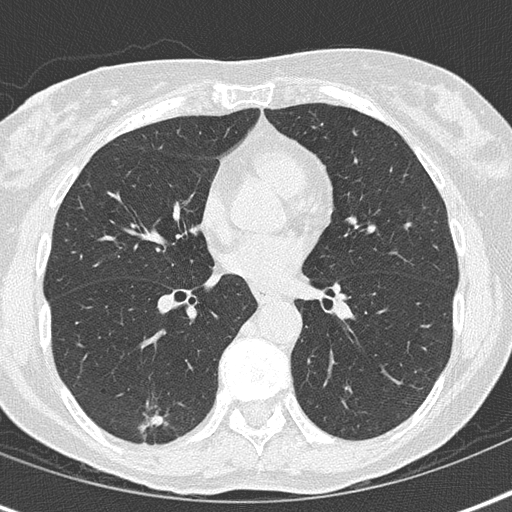
Low-dose screening chest CT, axial slice, baseline annual screen, lung window (W 1500 / L -600 HU), 2 mm slice thickness, lung (sharp) reconstruction kernel (B50f), slice 85 of 155 in the series. Female, age 69 years at enrolment.
- Expert reader's lesion annotation, bounding box (x1, y1, x2, y2) in pixels: (117, 399, 180, 456).
- The screening reader recorded 2 non-calcified nodules or masses ≥4 mm on this exam; which of them this box marks is not recorded.
- Official screen result: positive, change unspecified: nodule(s) >= 4 mm or enlarging nodule(s), mass(es), or other non-specific abnormalities suspicious for lung cancer.
- Later outcome: lung cancer diagnosed 476 days after this screen — adenocarcinoma, NOS, right lower lobe, moderately differentiated (G2), stage IA (AJCC 6th edition), 16 mm at pathology.